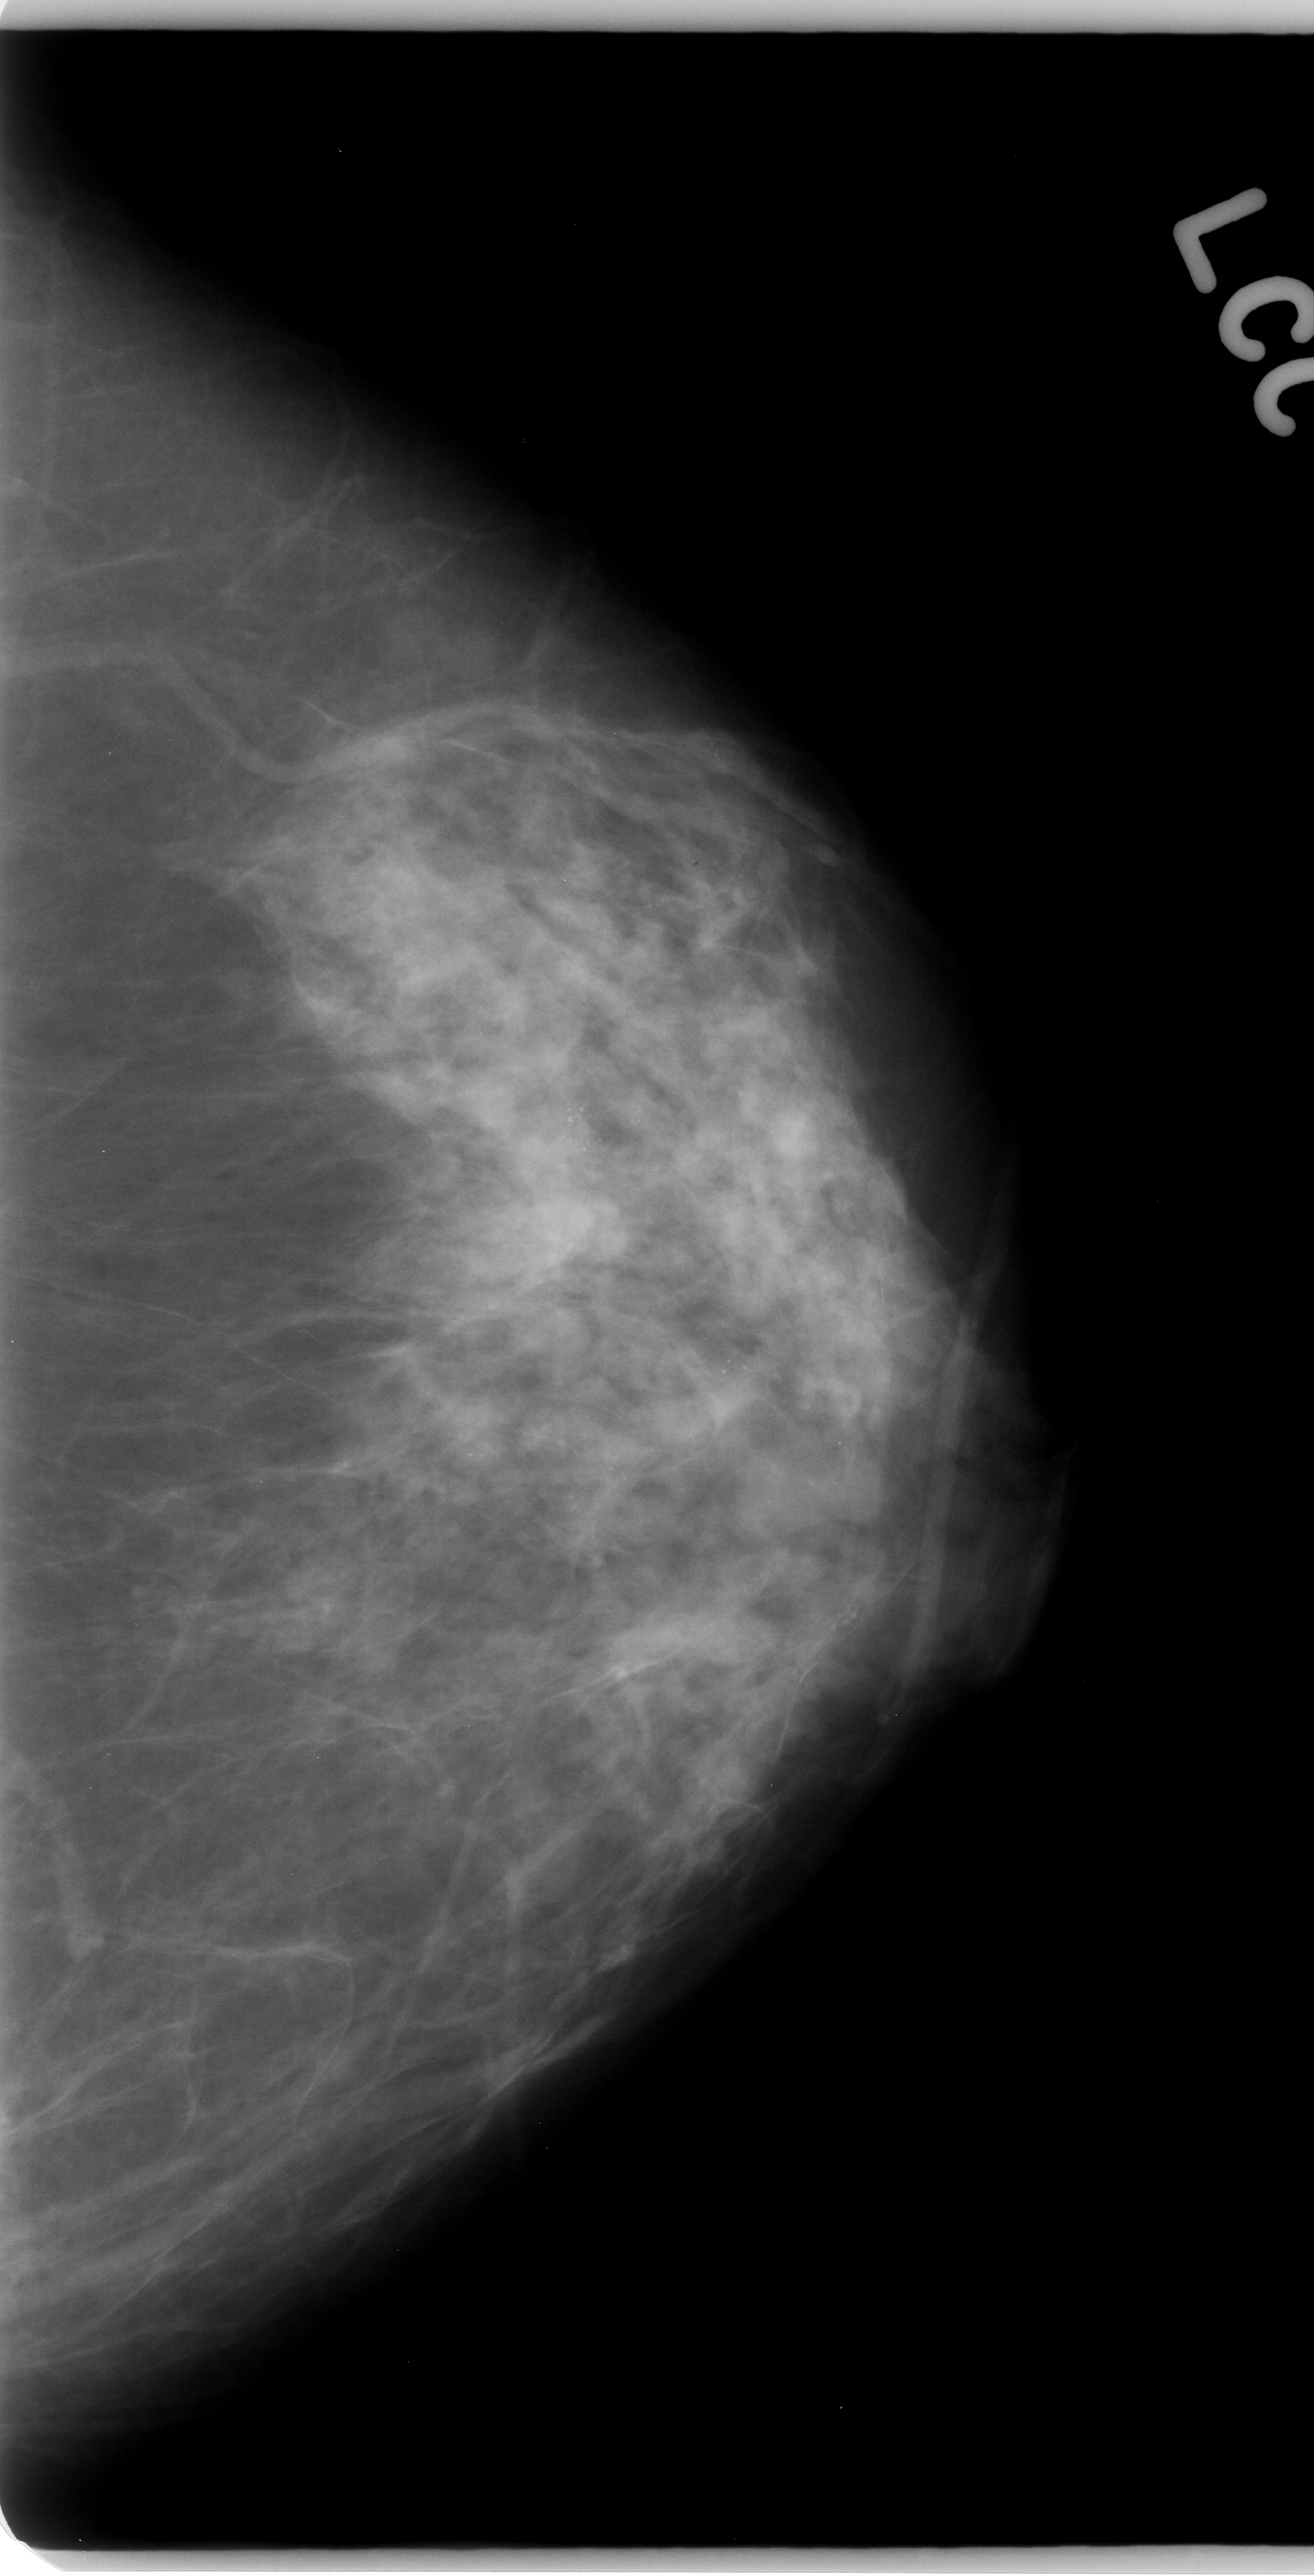
Digitized screen-film mammogram. Left breast. CC view. BI-RADS breast density category 2 (scale 1–4). 1314 × 2576 image matrix.
Marked abnormalities (boxes around the expert regions of interest):
- calcifications, morphology amorphous, distribution regional; BI-RADS assessment category 4; pathology result (as recorded, not read from the image): malignant: bounding box <130,864,957,1660> (left, top, right, bottom; pixels)